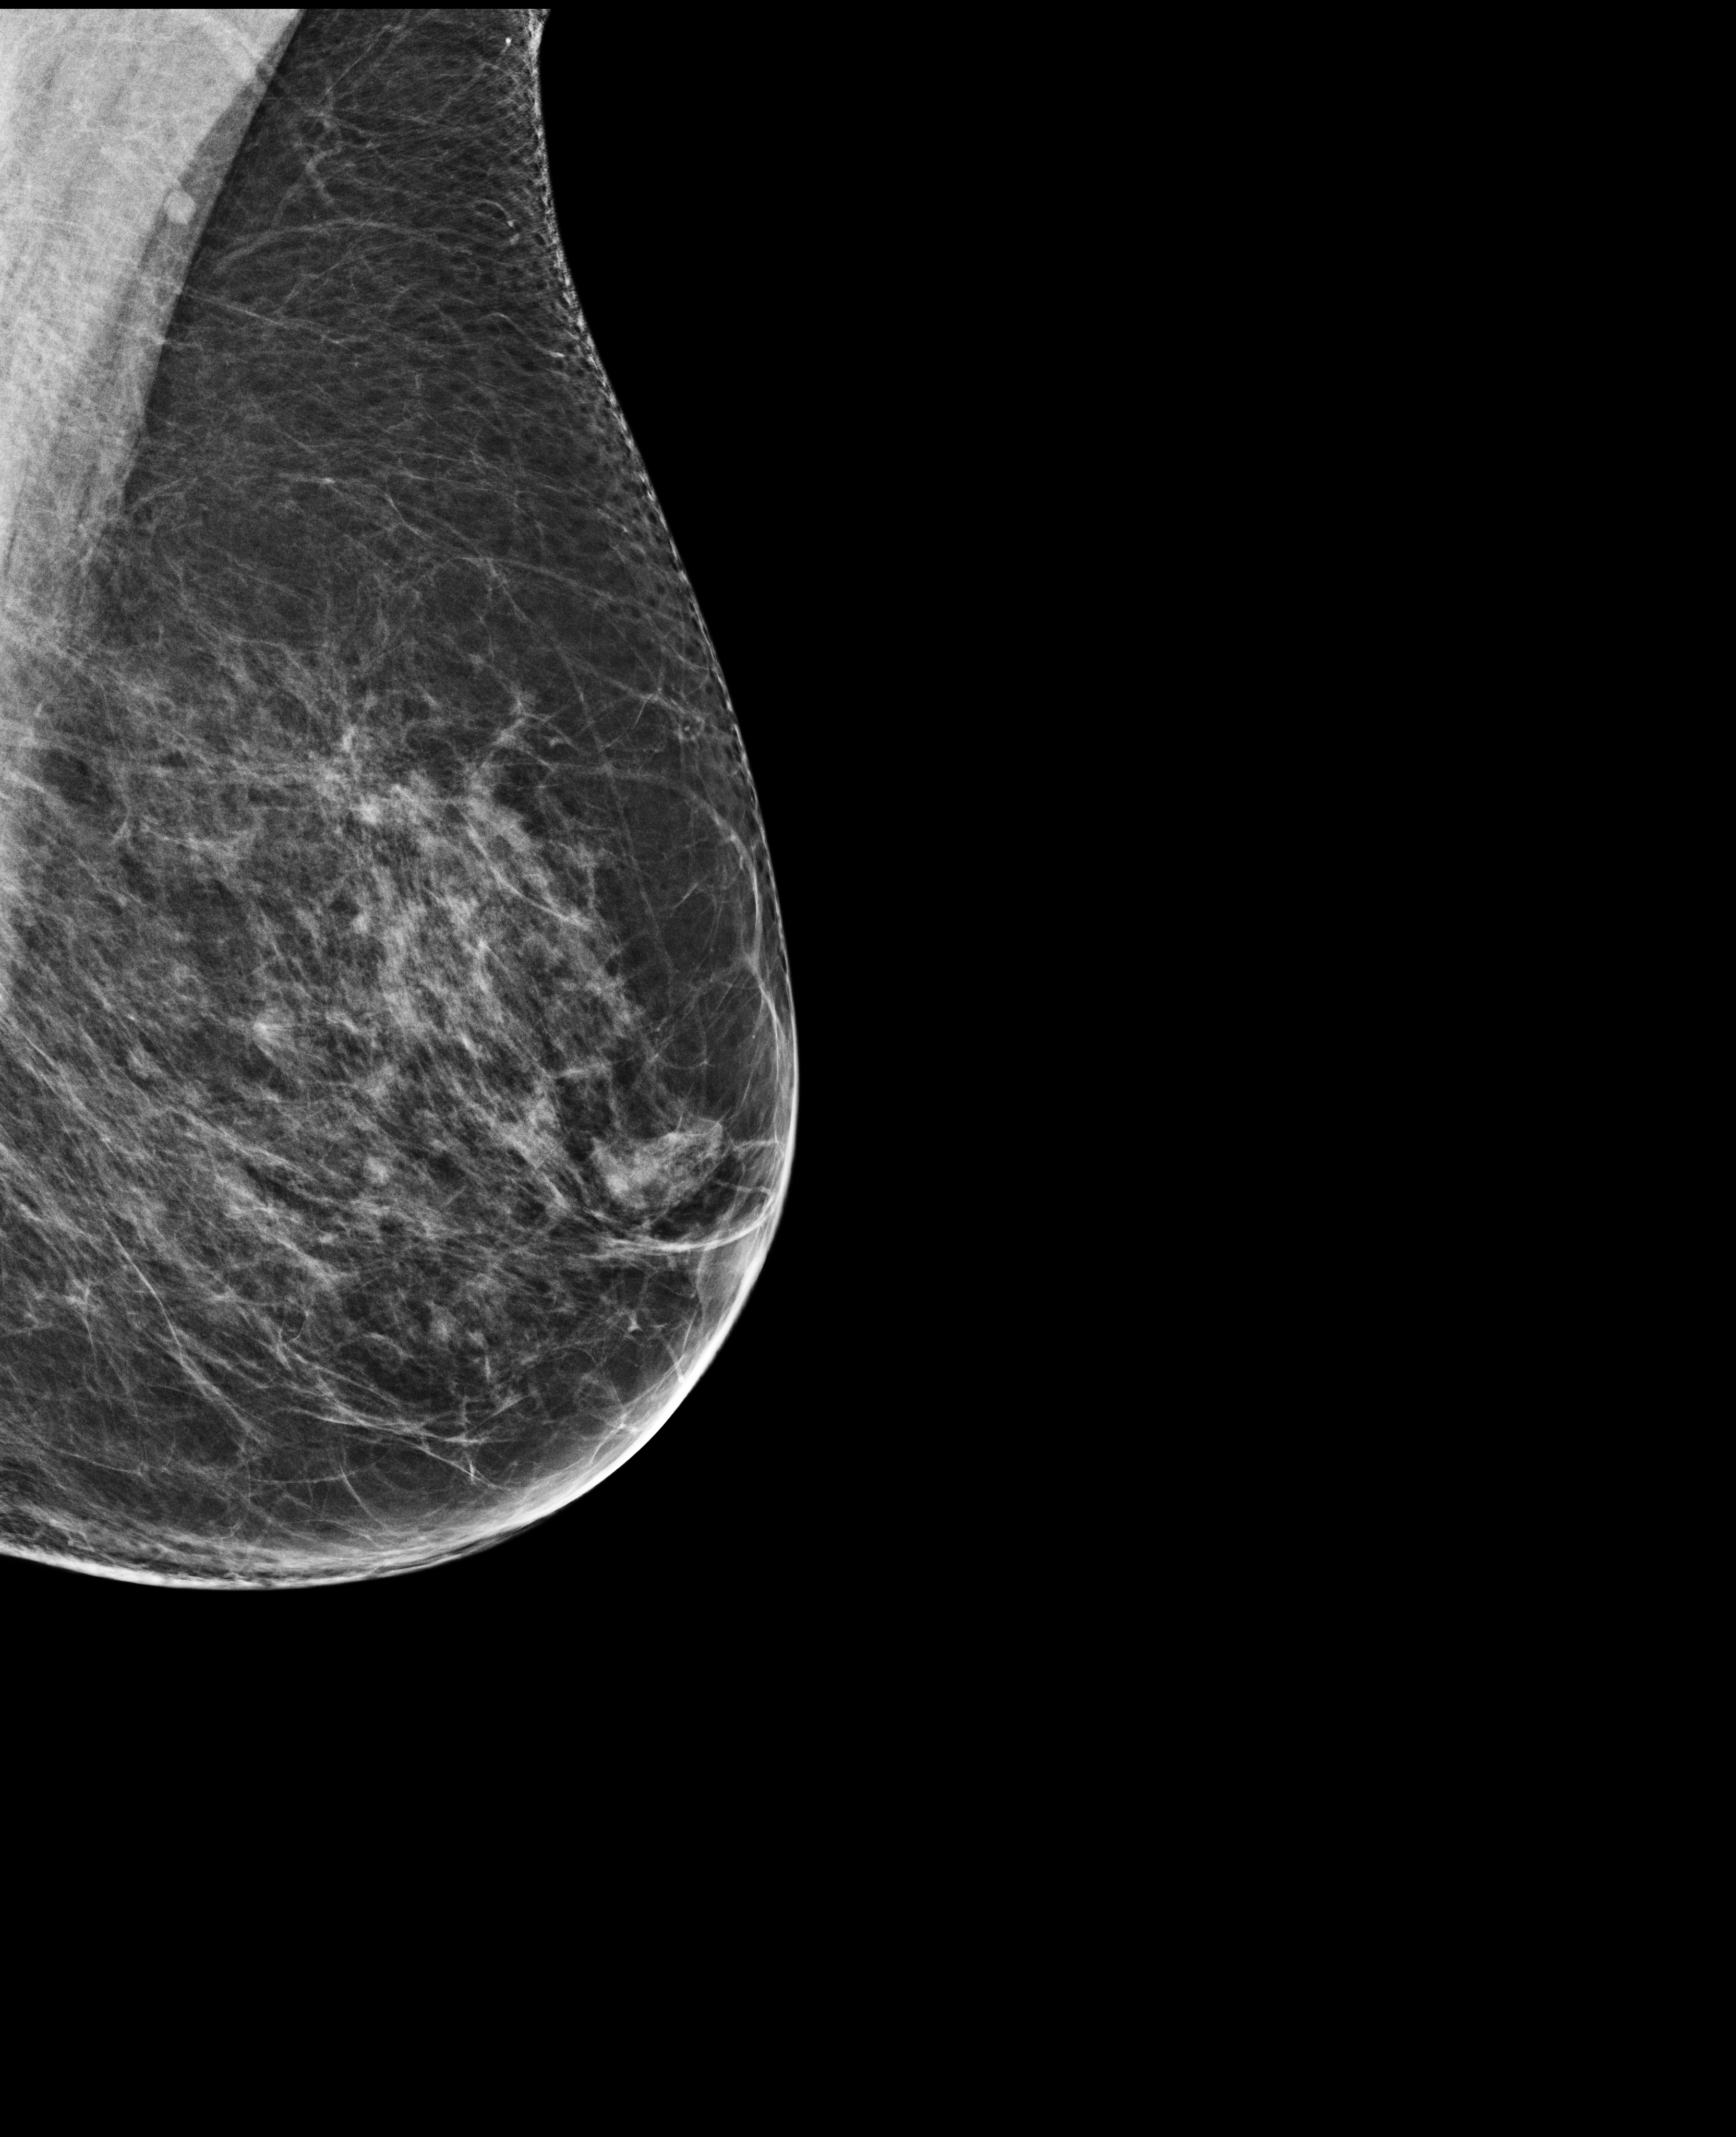
Annual screening mammography examination, compressed breast thickness 54 mm, system: Selenia Dimensions. Patient aged 68 years (female).
Image type: full-field digital mammogram. Breast: left. Projection: MLO view.